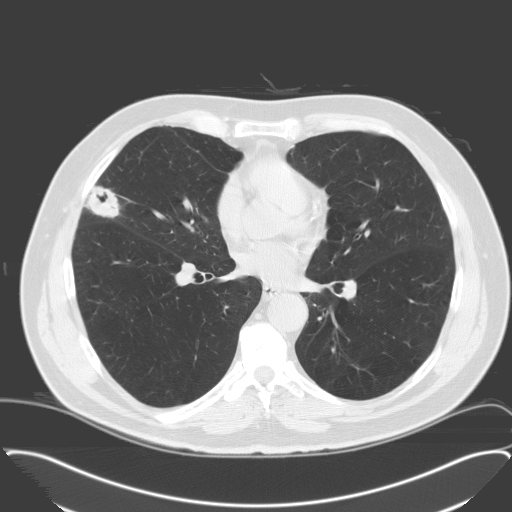
Low-dose screening chest CT, one axial slice; slice 87 of 174 in the series (ordered by position); 120 kVp; lung window (W 1500 / L -600 HU); 3.2 mm slice thickness; 512 × 512 image matrix, field of view 400 × 400 mm.
Structures marked on this image (outlined manually by an expert reader):
- lesion 1 (tumor, middle lobe of right lung): bounding box <86,187,119,217> (left, top, right, bottom; pixels)